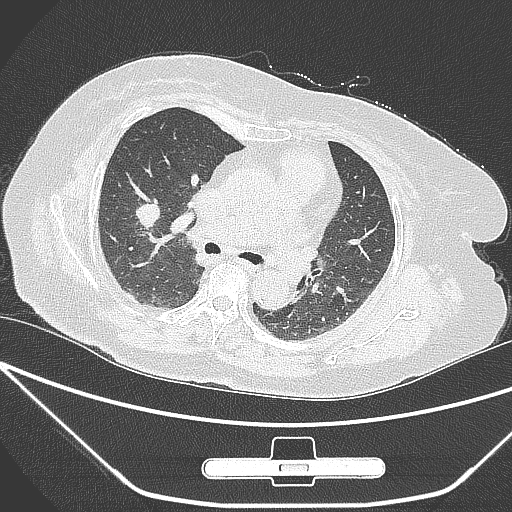
Chest CT, one axial slice; position 161 of 245 along the scan axis; 120 kVp; lung window (W 1500 / L -600 HU); 512 × 512 image matrix, field of view 365 × 365 mm. Female patient, age 65 years. From the clinical record (not read from this slice): clinical TNM (as recorded): T1c N0 M0.
Structures marked on this image (rectangle marked by the reading radiologist):
- lung tumour (recorded histology: adenocarcinoma): box from (x=119, y=195) to (x=163, y=242) px